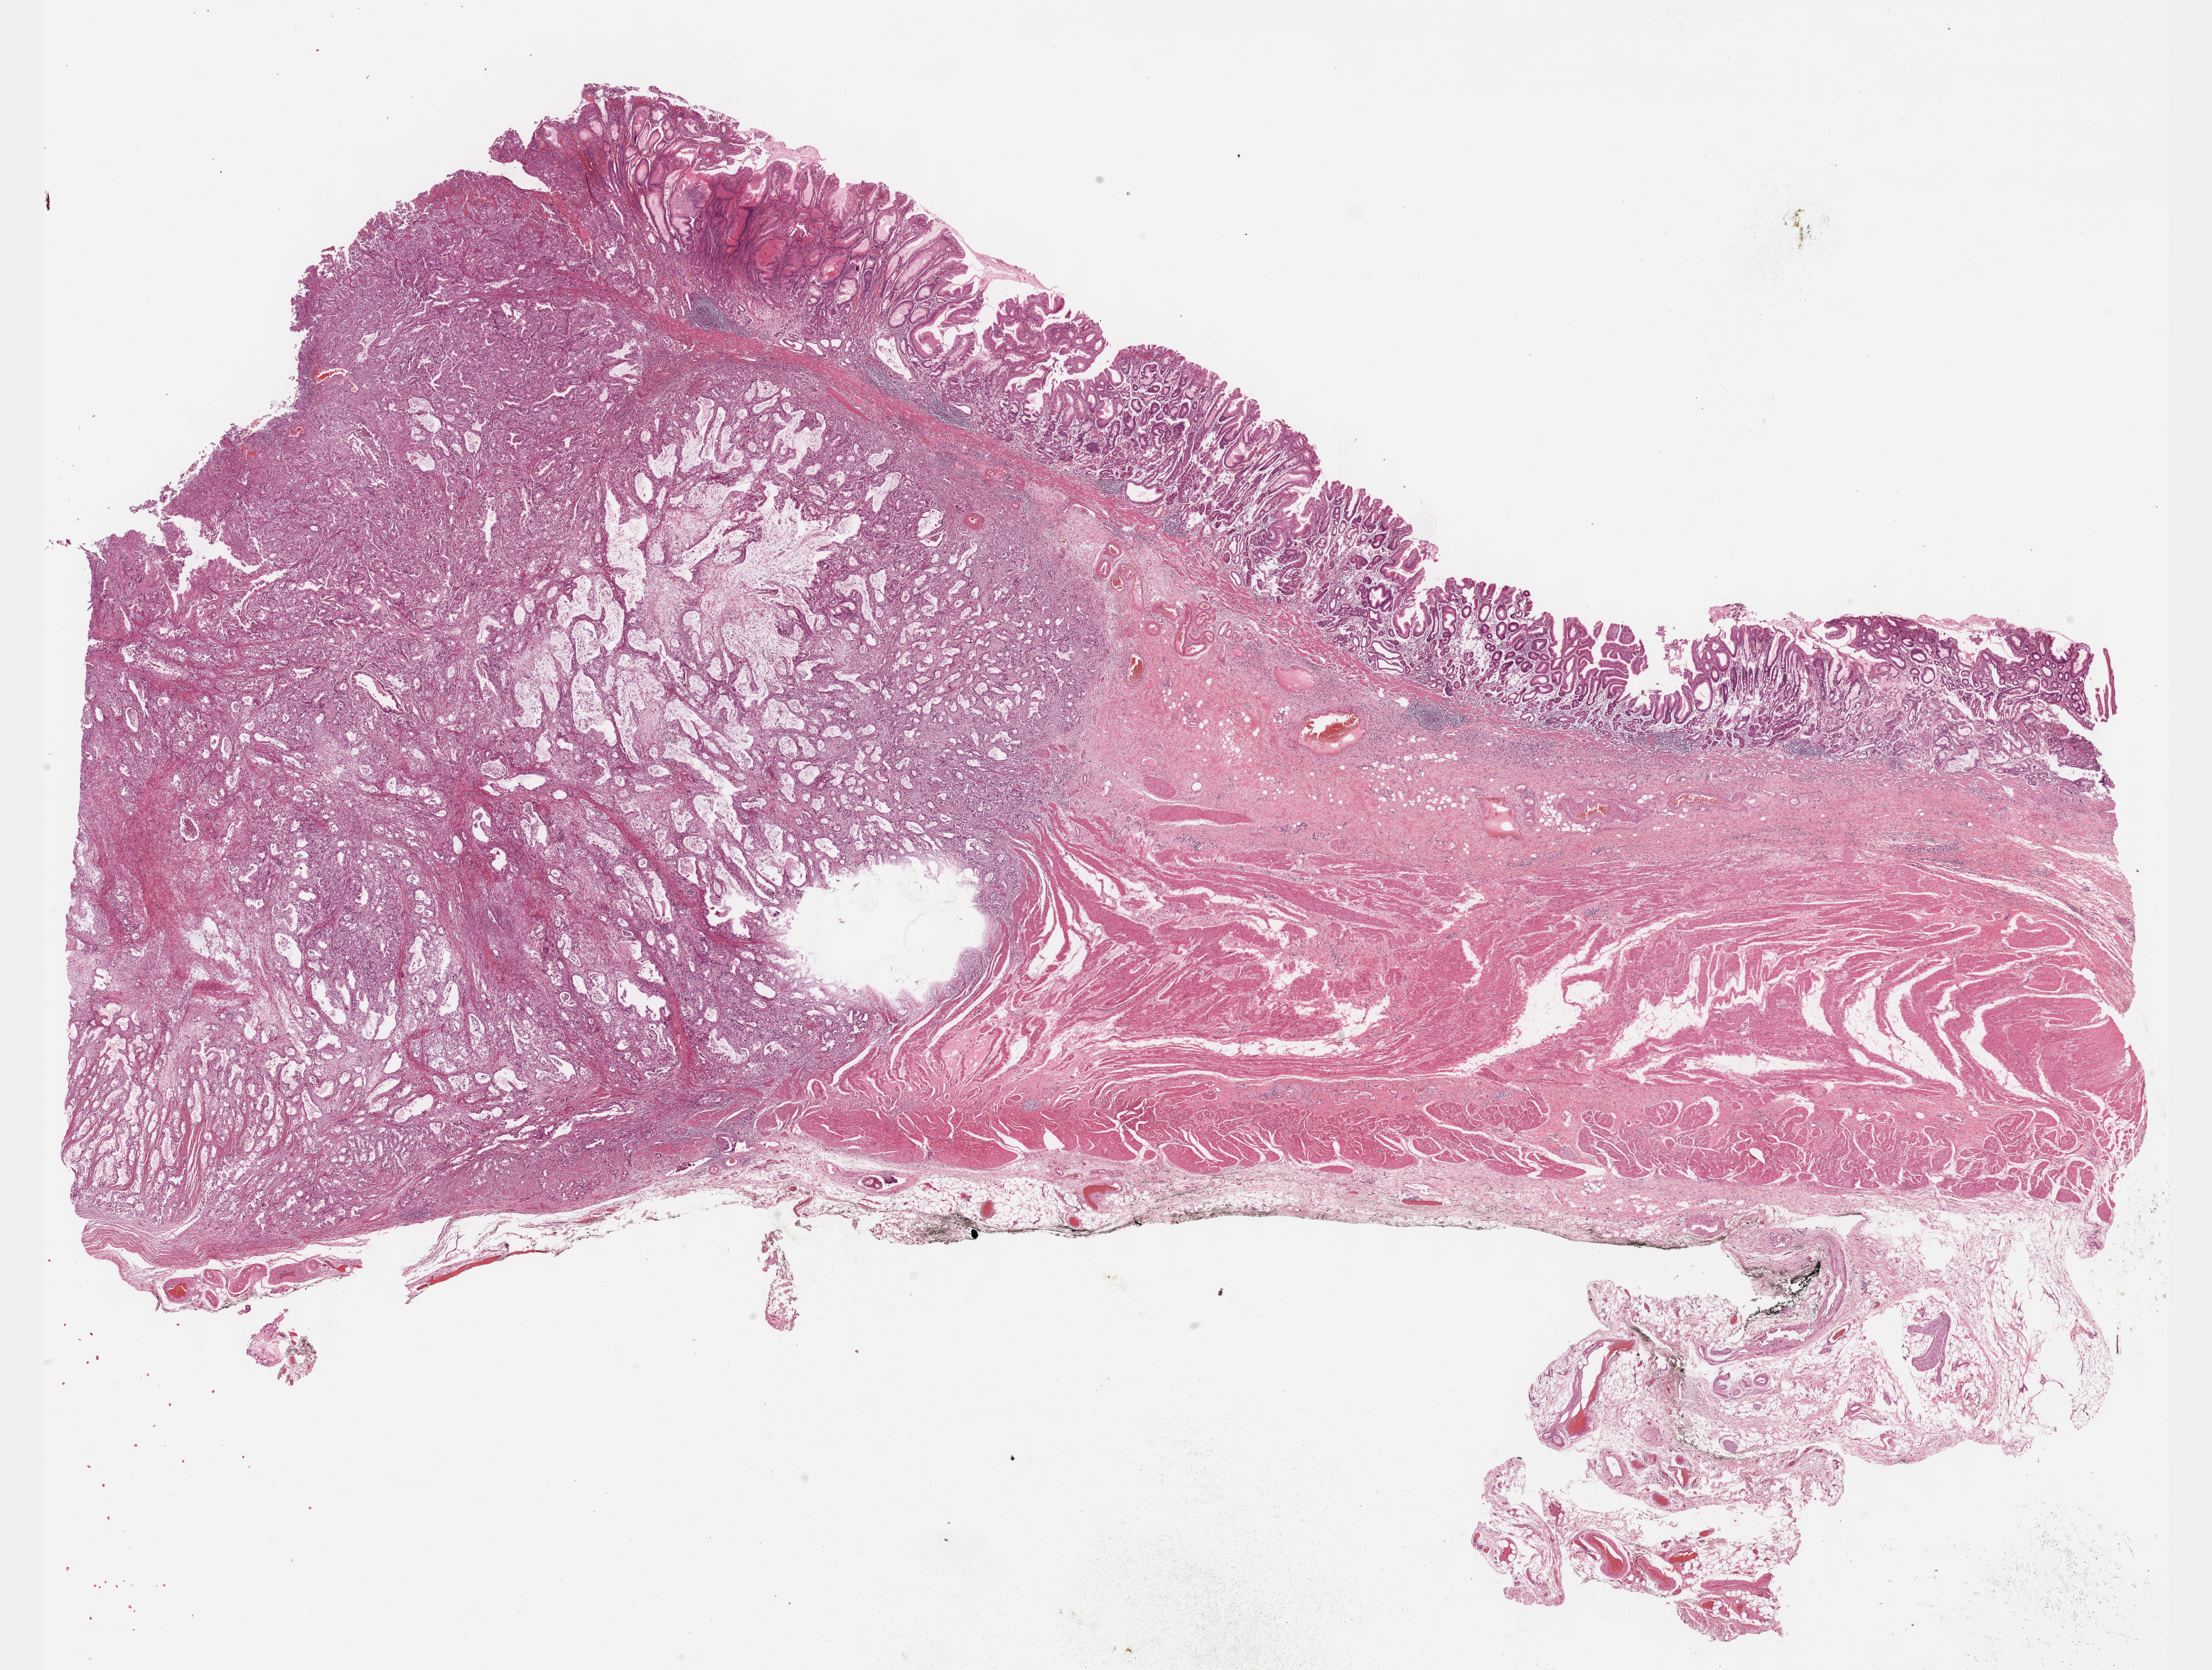
Digitized H&E tissue section (whole slide) — shown as a low-resolution overview of the whole scanned area (about 25.1 x 19.0 mm, slide scanned at 40x); formalin-fixed paraffin-embedded (FFPE) diagnostic section; sample: primary tumour, stomach. Patient: male, age at initial diagnosis 76 years. Histologic grade: G2 (moderately differentiated).
• pathologic diagnosis: Adenocarcinoma, intestinal type
• lymph nodes positive (case pathology): 1 of 11 examined
• AJCC pathologic stage: IIIA (6th edition)
• TNM: T3 N1 M0